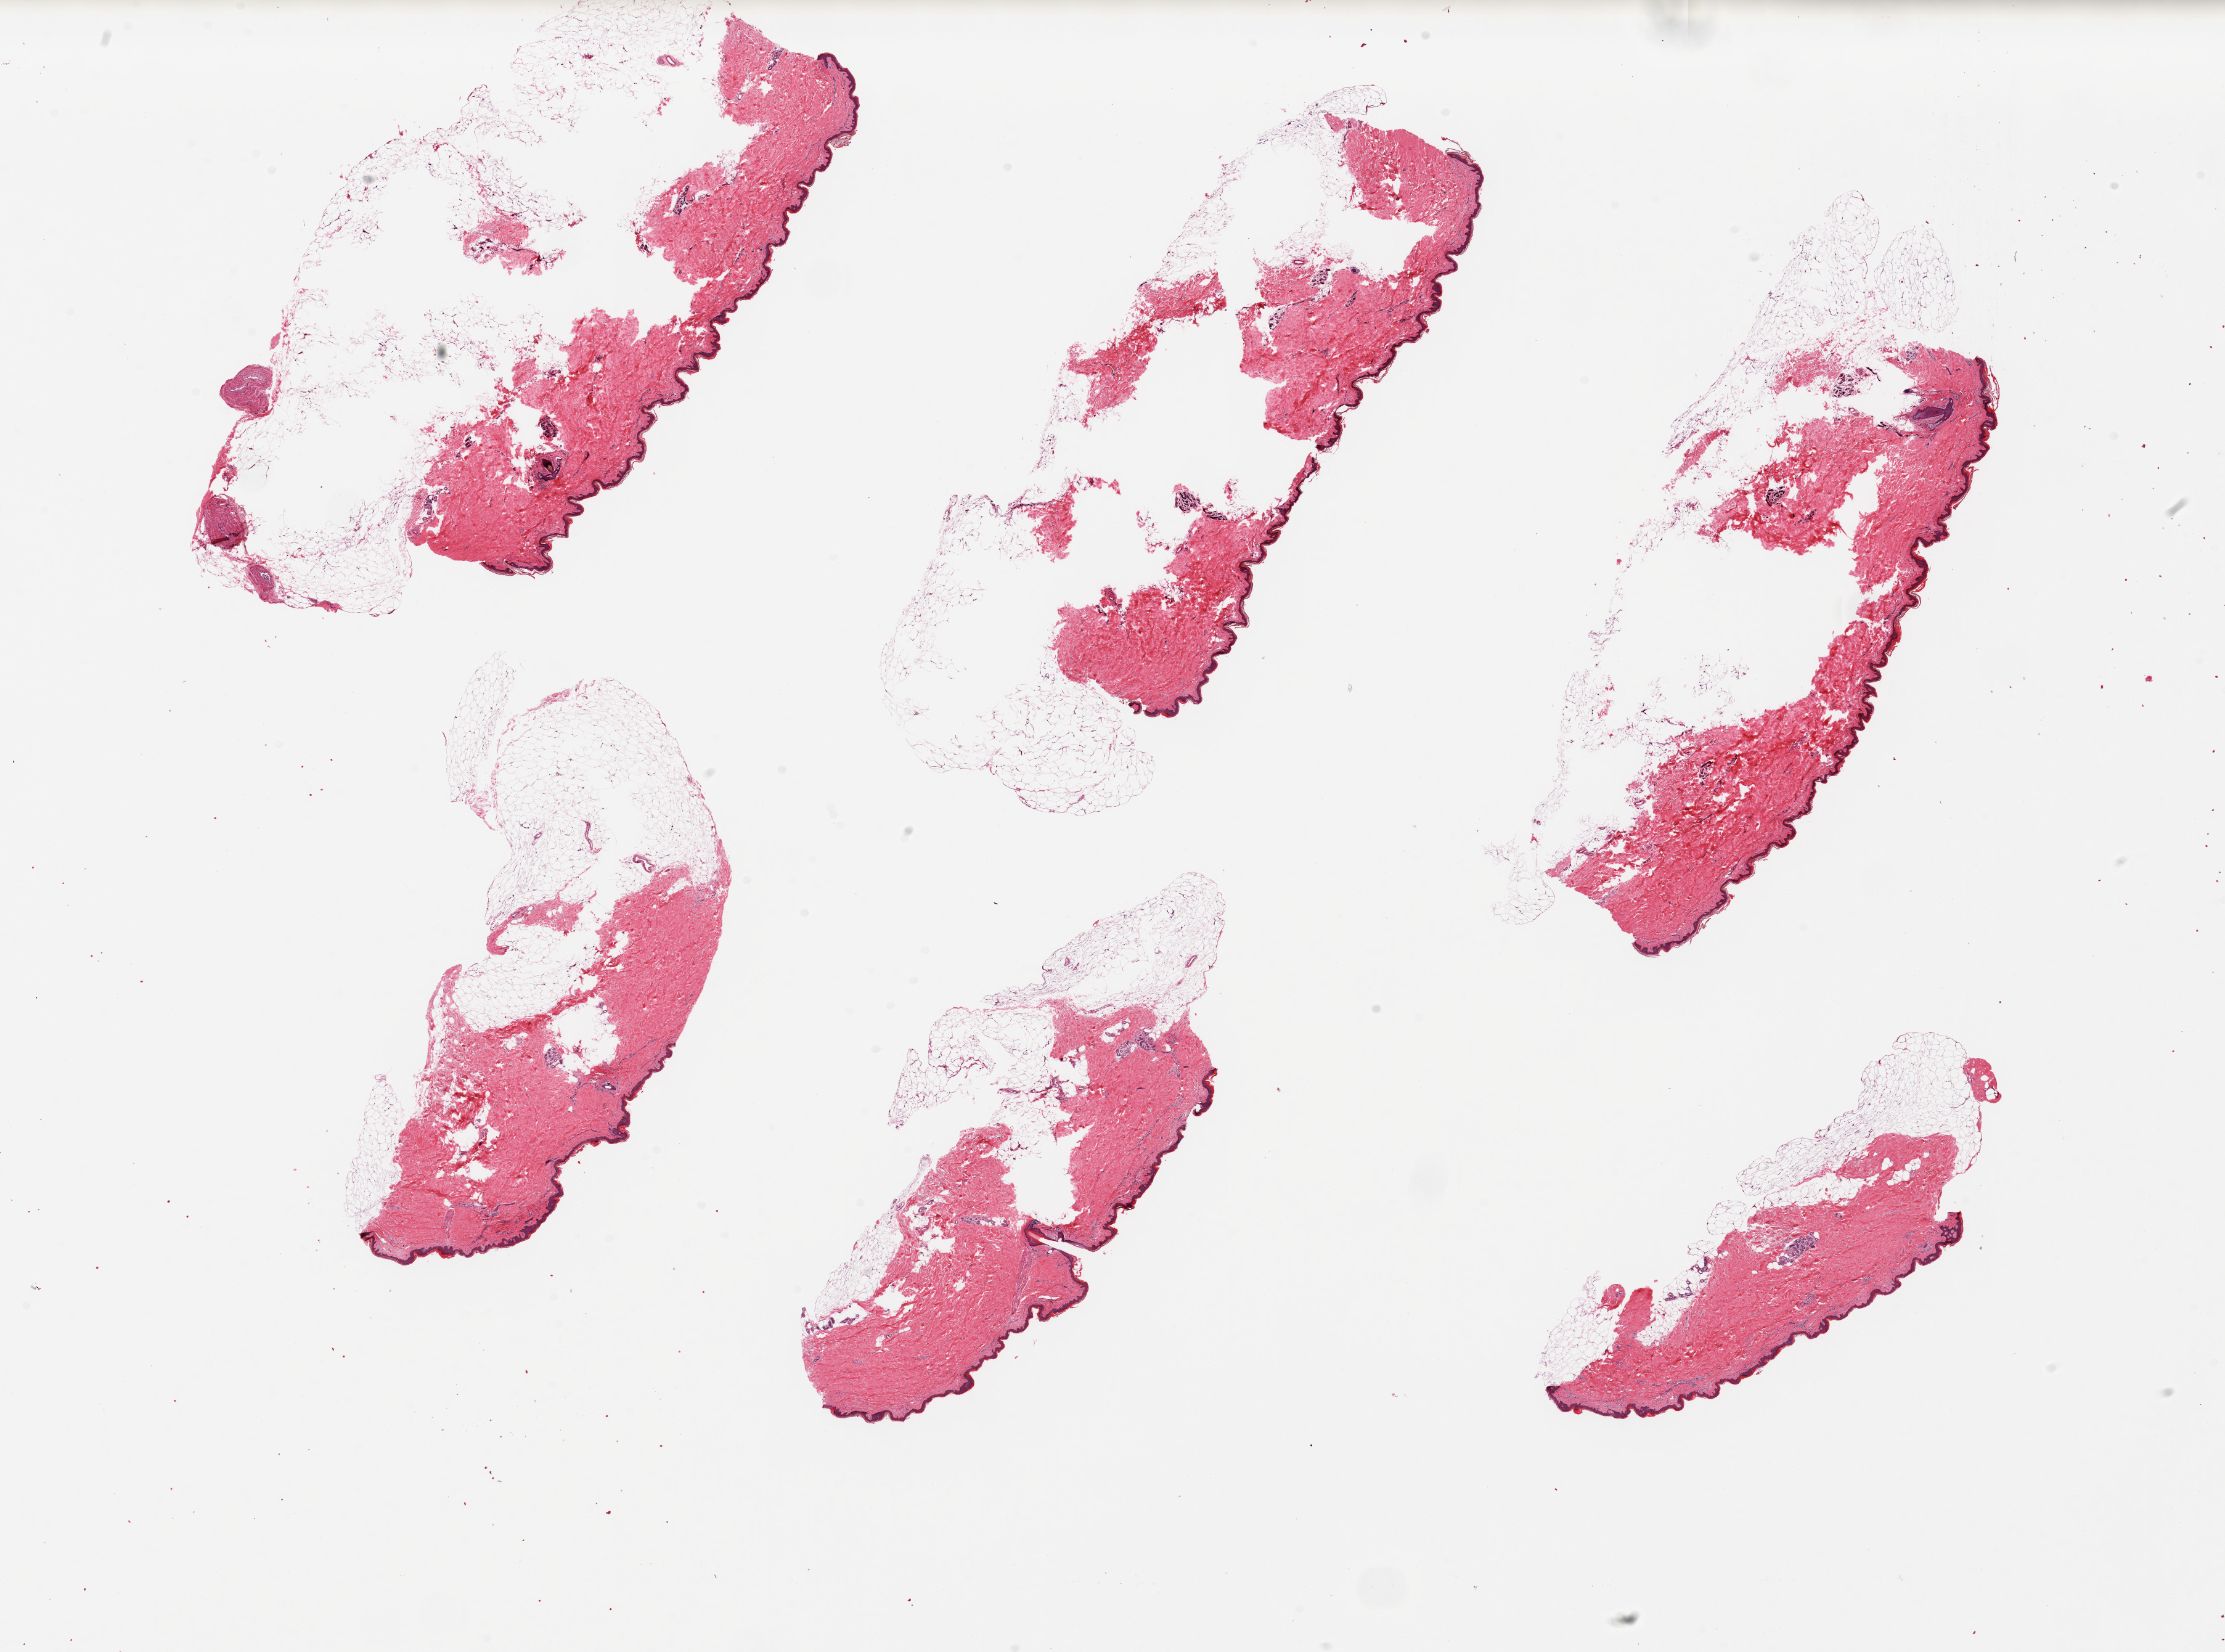
Digitized hematoxylin and eosin (H&E)-stained section, brightfield — low-resolution overview of the scanned area, about 28.5 x 21.2 mm, PAXgene-fixed paraffin-embedded (PFPE) section, section of skin of lower leg (target tissue), tissue donor sample. Donor sex: male.
Pathologist's review note for this sample: 6 pieces ~8x3mm; Fat is ~50% of all sections; Squamous mucosa is ~2% of thickness; Non adipose components by line in representative sections for guidance.